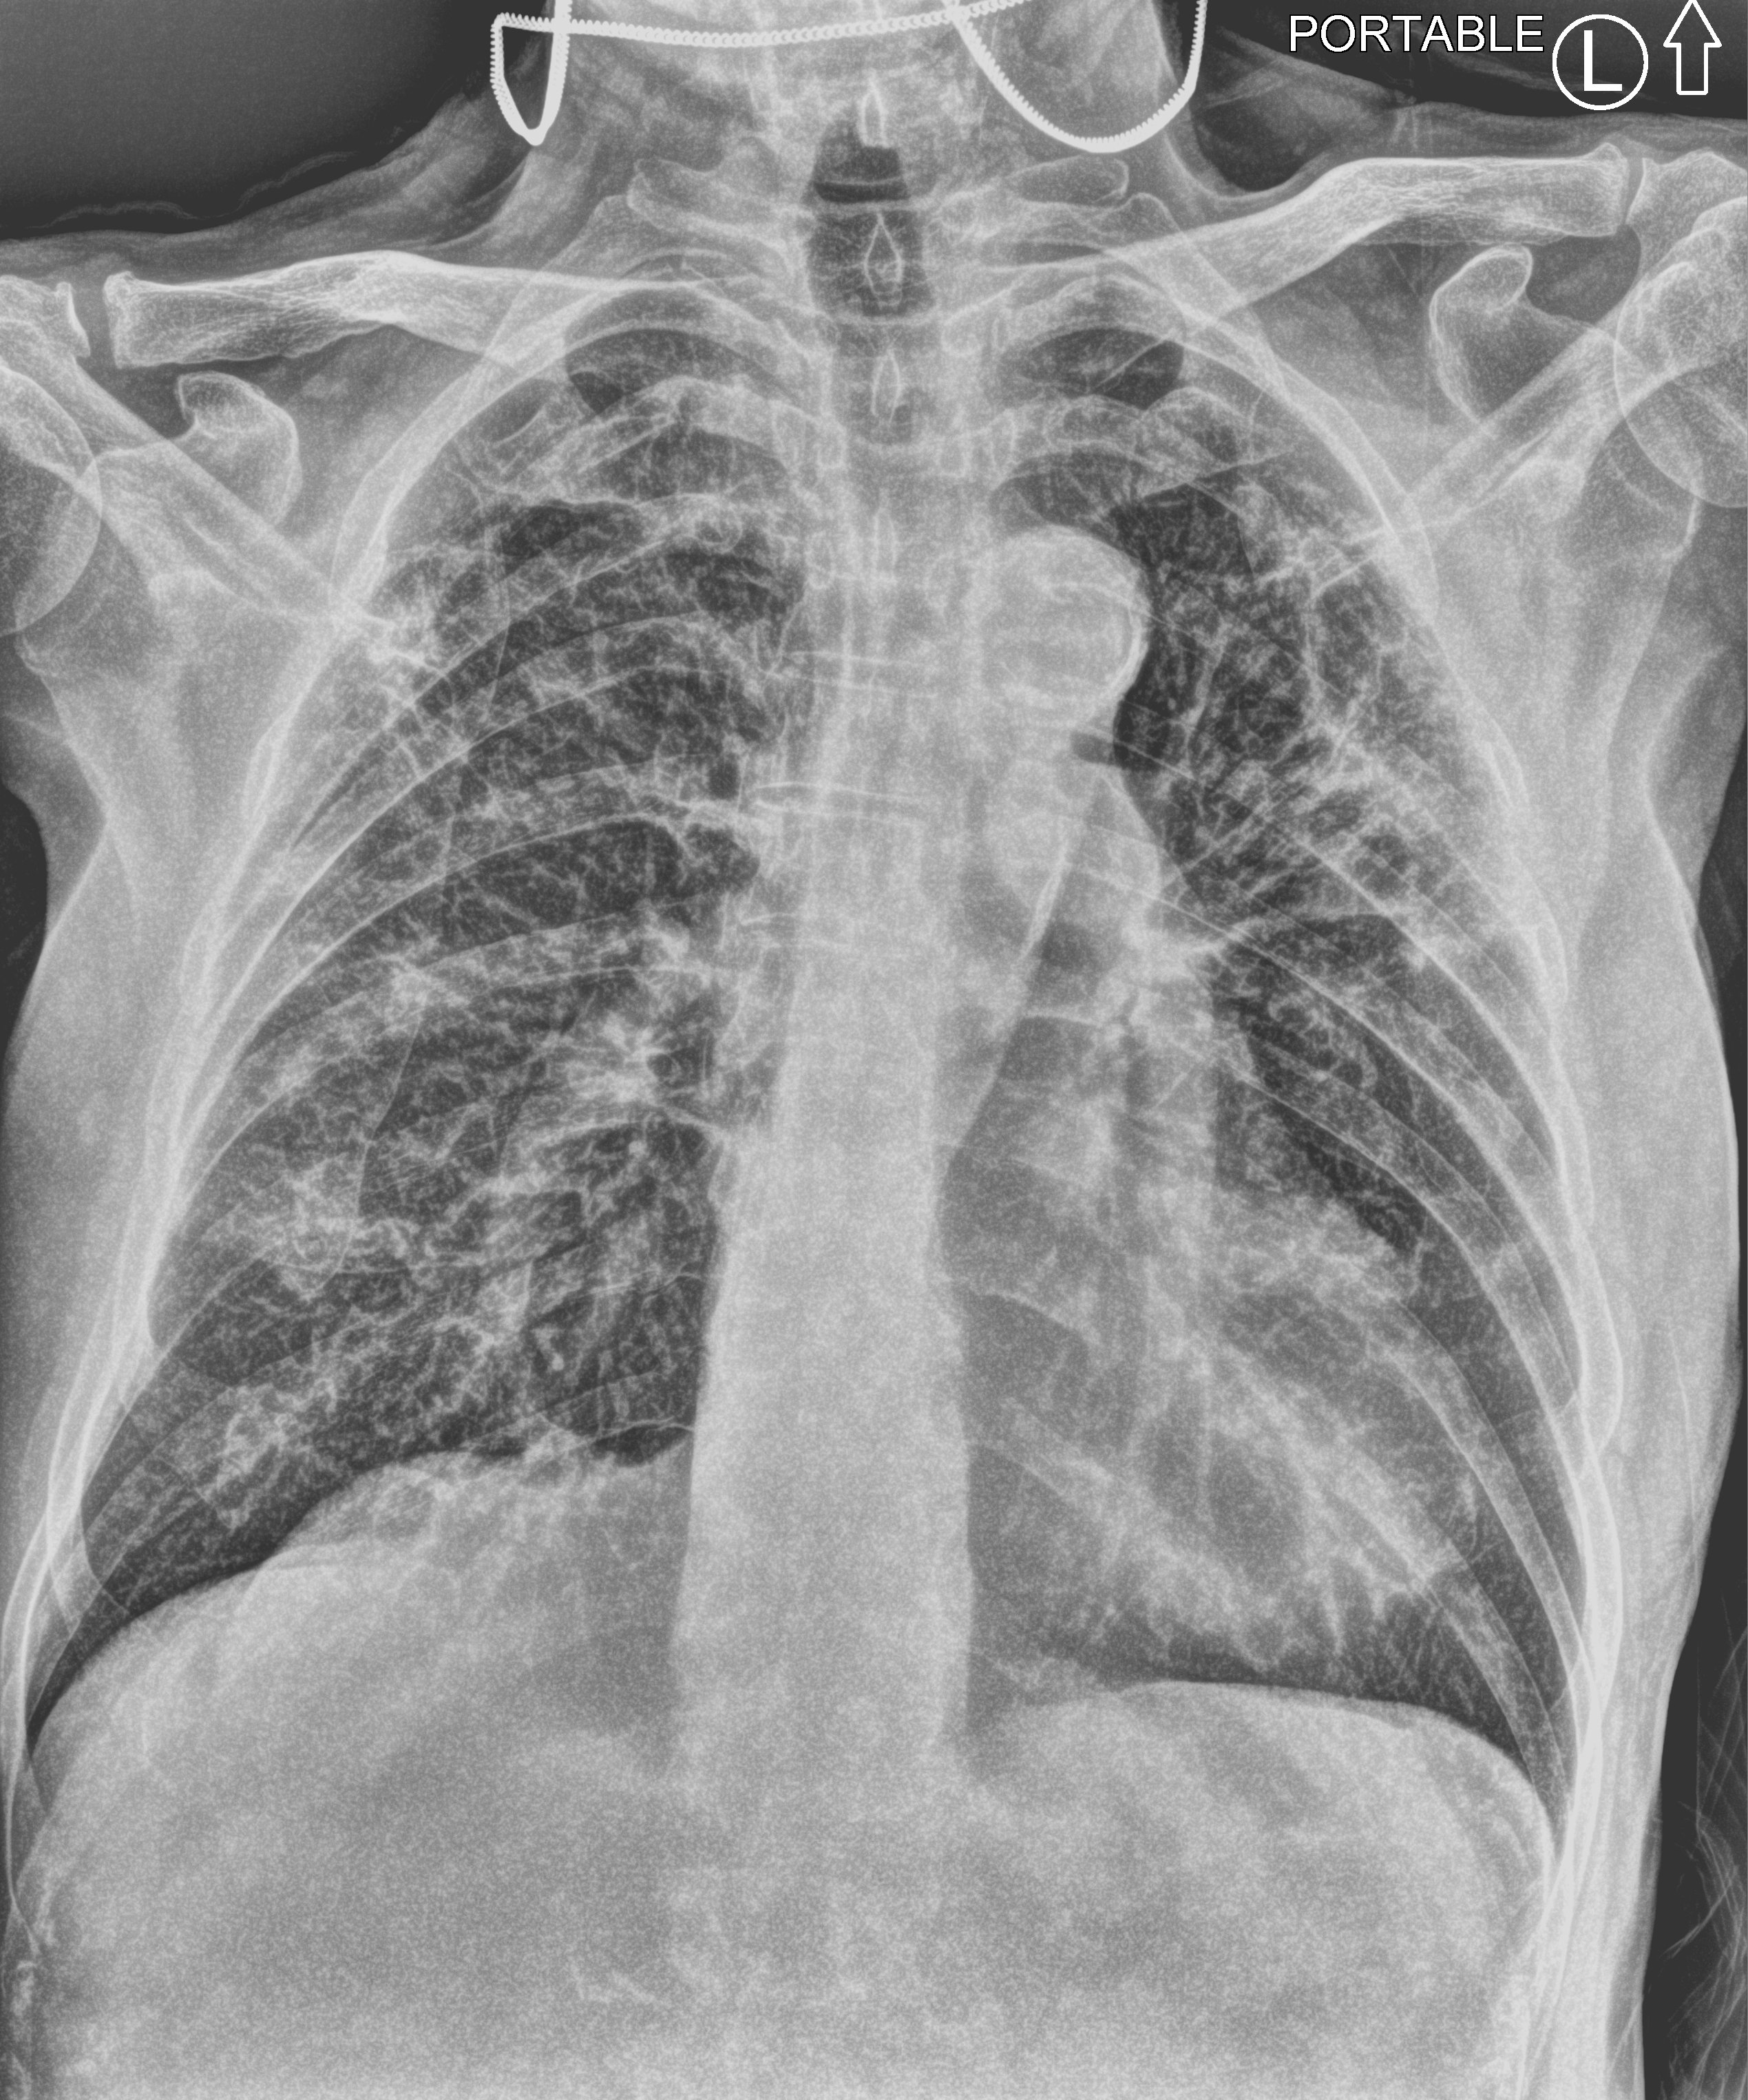
Bedside chest radiograph (computed radiography), anteroposterior (AP) projection. Patient hospitalised with COVID-19; male, aged 75–90 years.
Admission-level facts for this patient (not findings on this image; timing relative to this image not recorded): mechanically ventilated during this hospital stay: no.